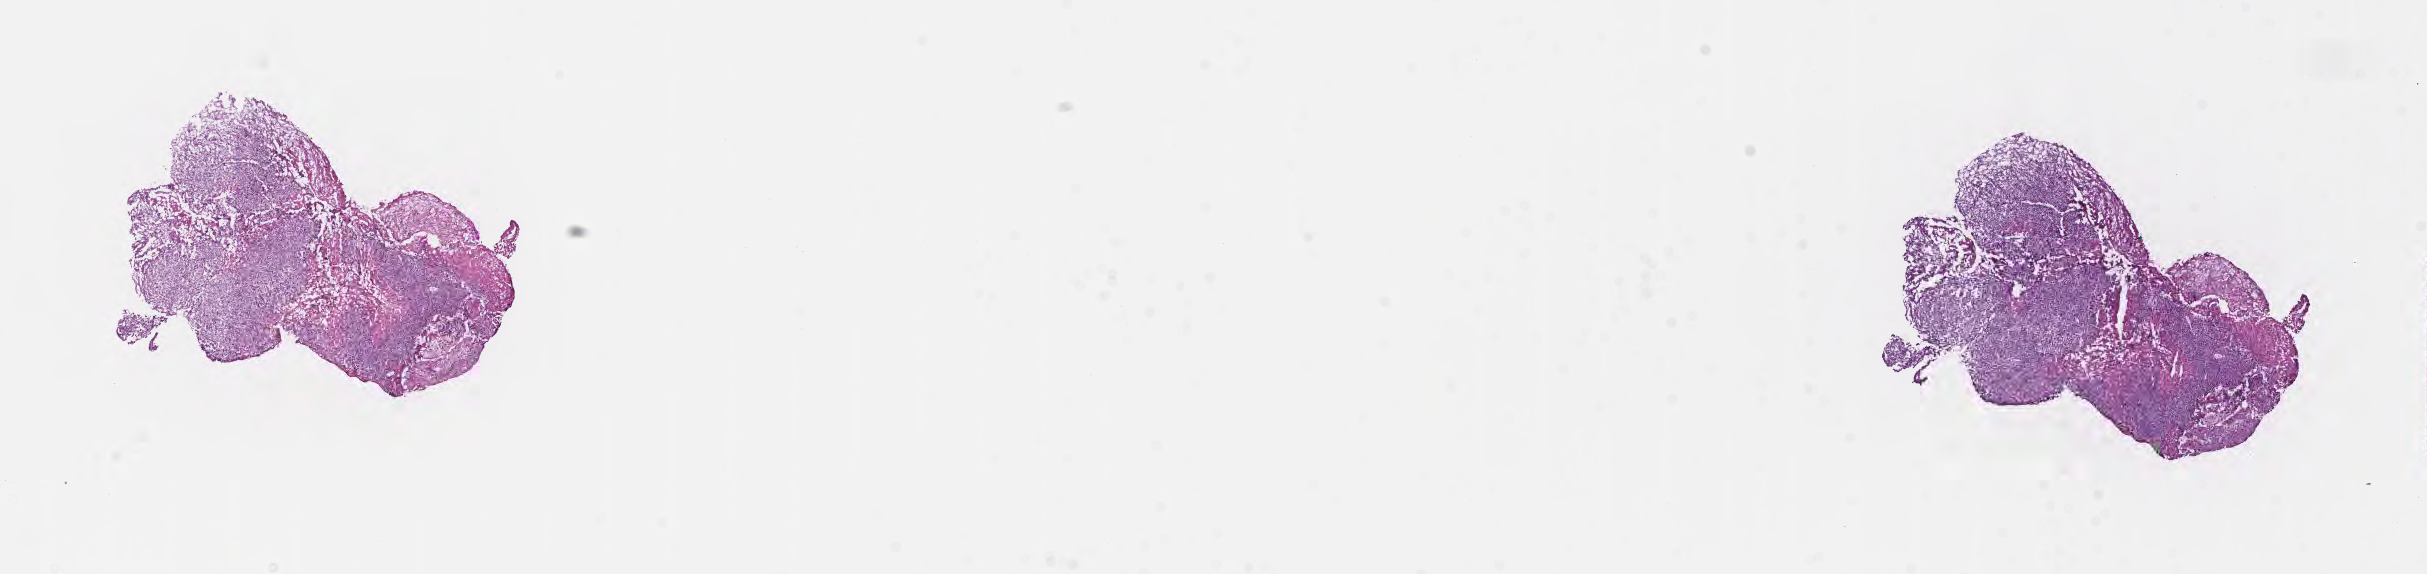
Digitized hematoxylin and eosin (H&E)-stained section — whole scanned area (about 19.6 x 4.6 mm) shown as a low-resolution overview. Frozen section (tissue freezing medium). Metastatic tumor tissue, resected from brain. Male, age 31 years at initial diagnosis. Composition of this section per pathologist review: tumor cells 70%, tumor nuclei 95%, stromal cells 0%, necrosis 30%, normal cells 0%. Infiltration values recorded for this section: lymphocyte infiltration 0%, monocyte infiltration 0%, neutrophil infiltration 0%.
Patient diagnosis (primary): Malignant melanoma, NOS. Section: bottom of the tissue portion.